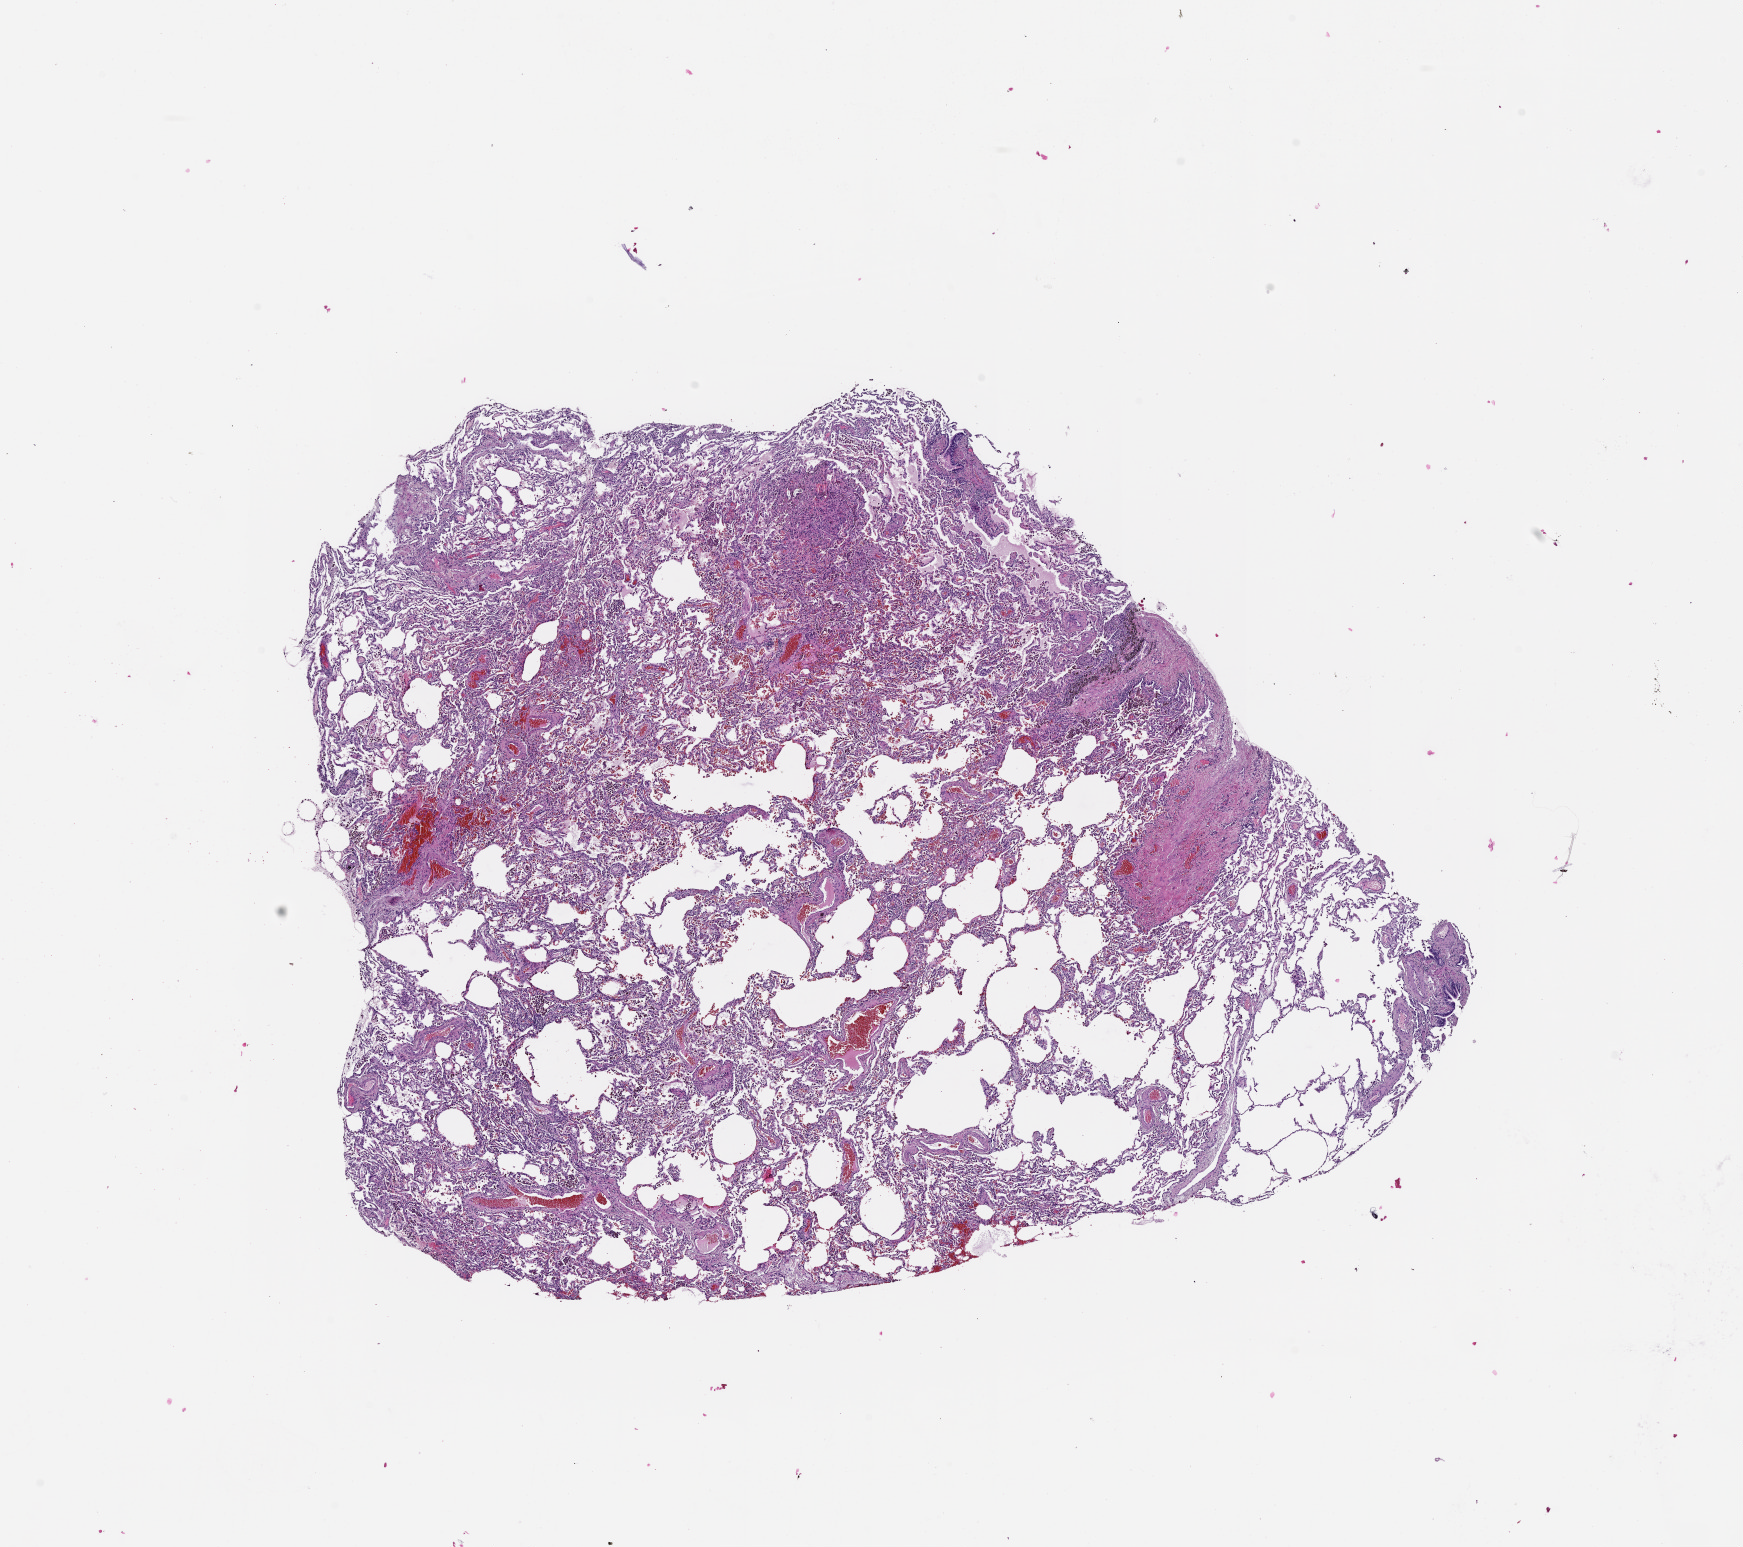
H&E-stained whole-slide image, shown as a low-resolution overview of the whole scanned area (about 14.0 x 12.5 mm, acquisition: 20x scan); lung, normal (non-tumour) tissue. 55-year-old male patient.
This section: normal (non-tumour) tissue from the same patient. Patient diagnosis (cohort enrolment): squamous cell carcinoma (lung).